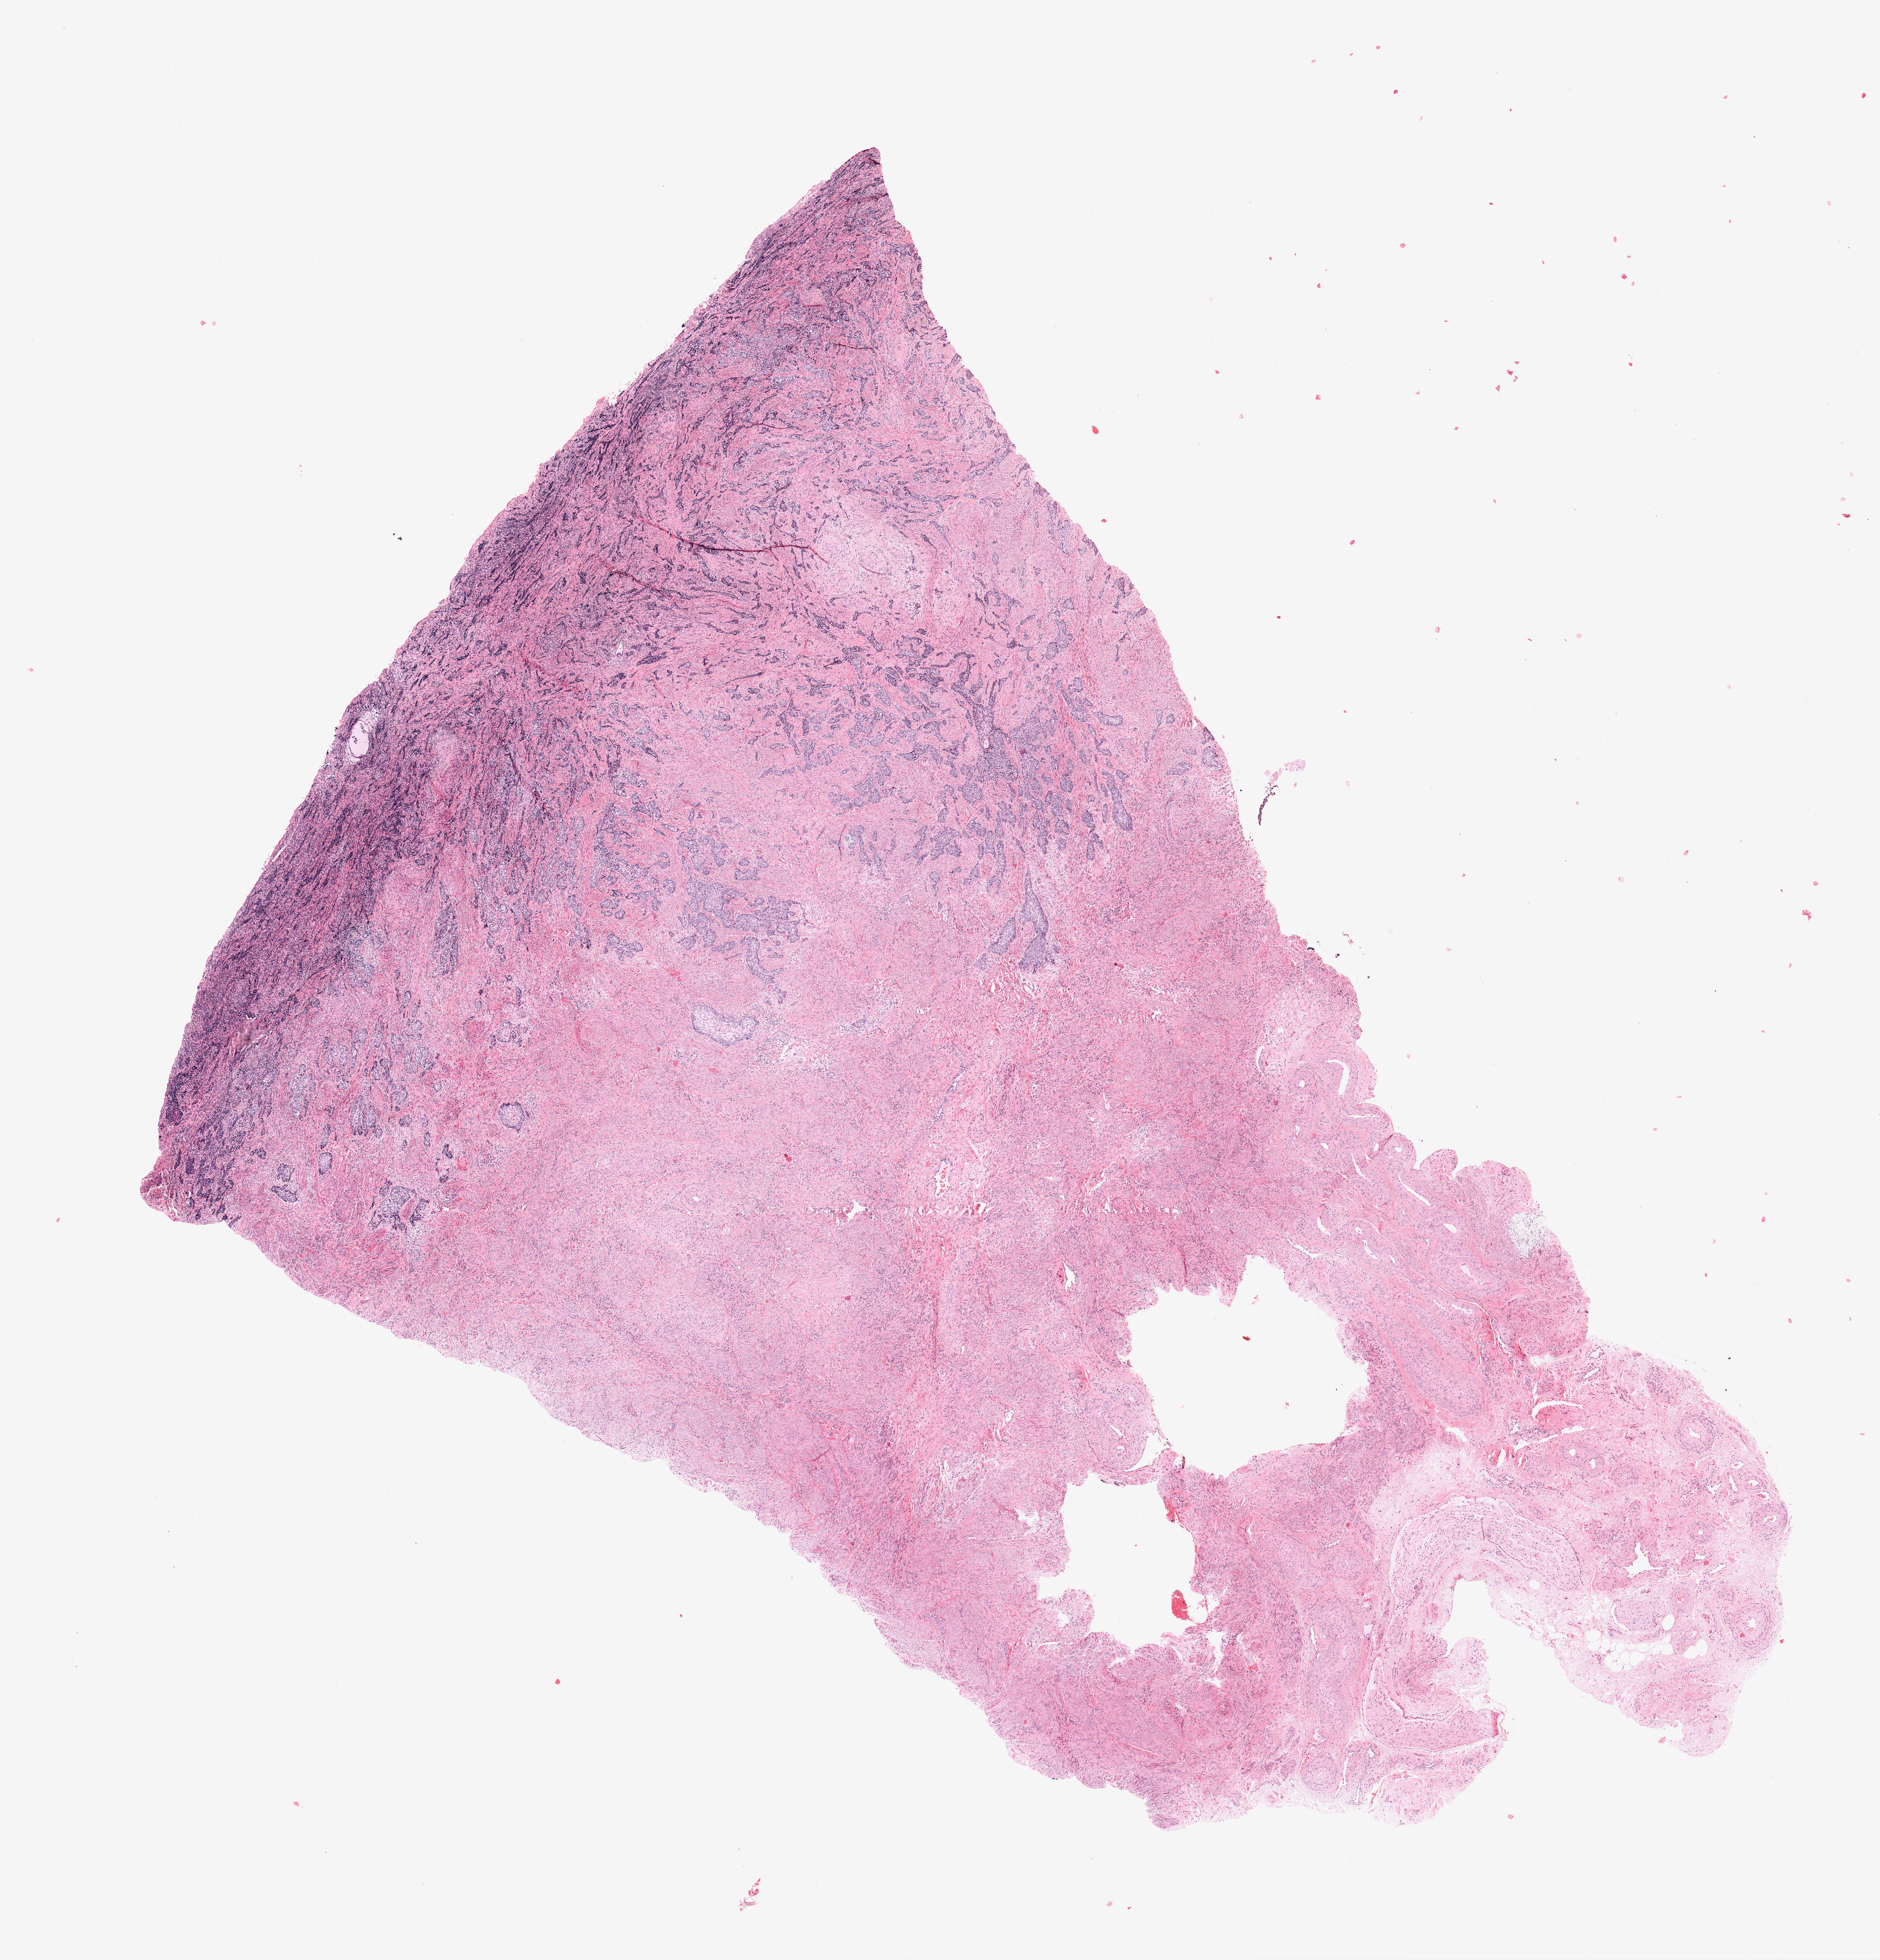
H&E-stained whole-slide image, low-resolution overview of the scanned area, about 12.0 x 12.5 mm (from a 20x scan). Formalin-fixed paraffin-embedded (FFPE) diagnostic section. Cervix, primary tumour sample. Female, age 60 years at initial diagnosis. Histologic grade: G2 (moderately differentiated).
FIGO stage: IA1. Histologic diagnosis: Squamous cell carcinoma, NOS (cervix uteri). Lymph nodes positive (case pathology): 0 of 18 examined.